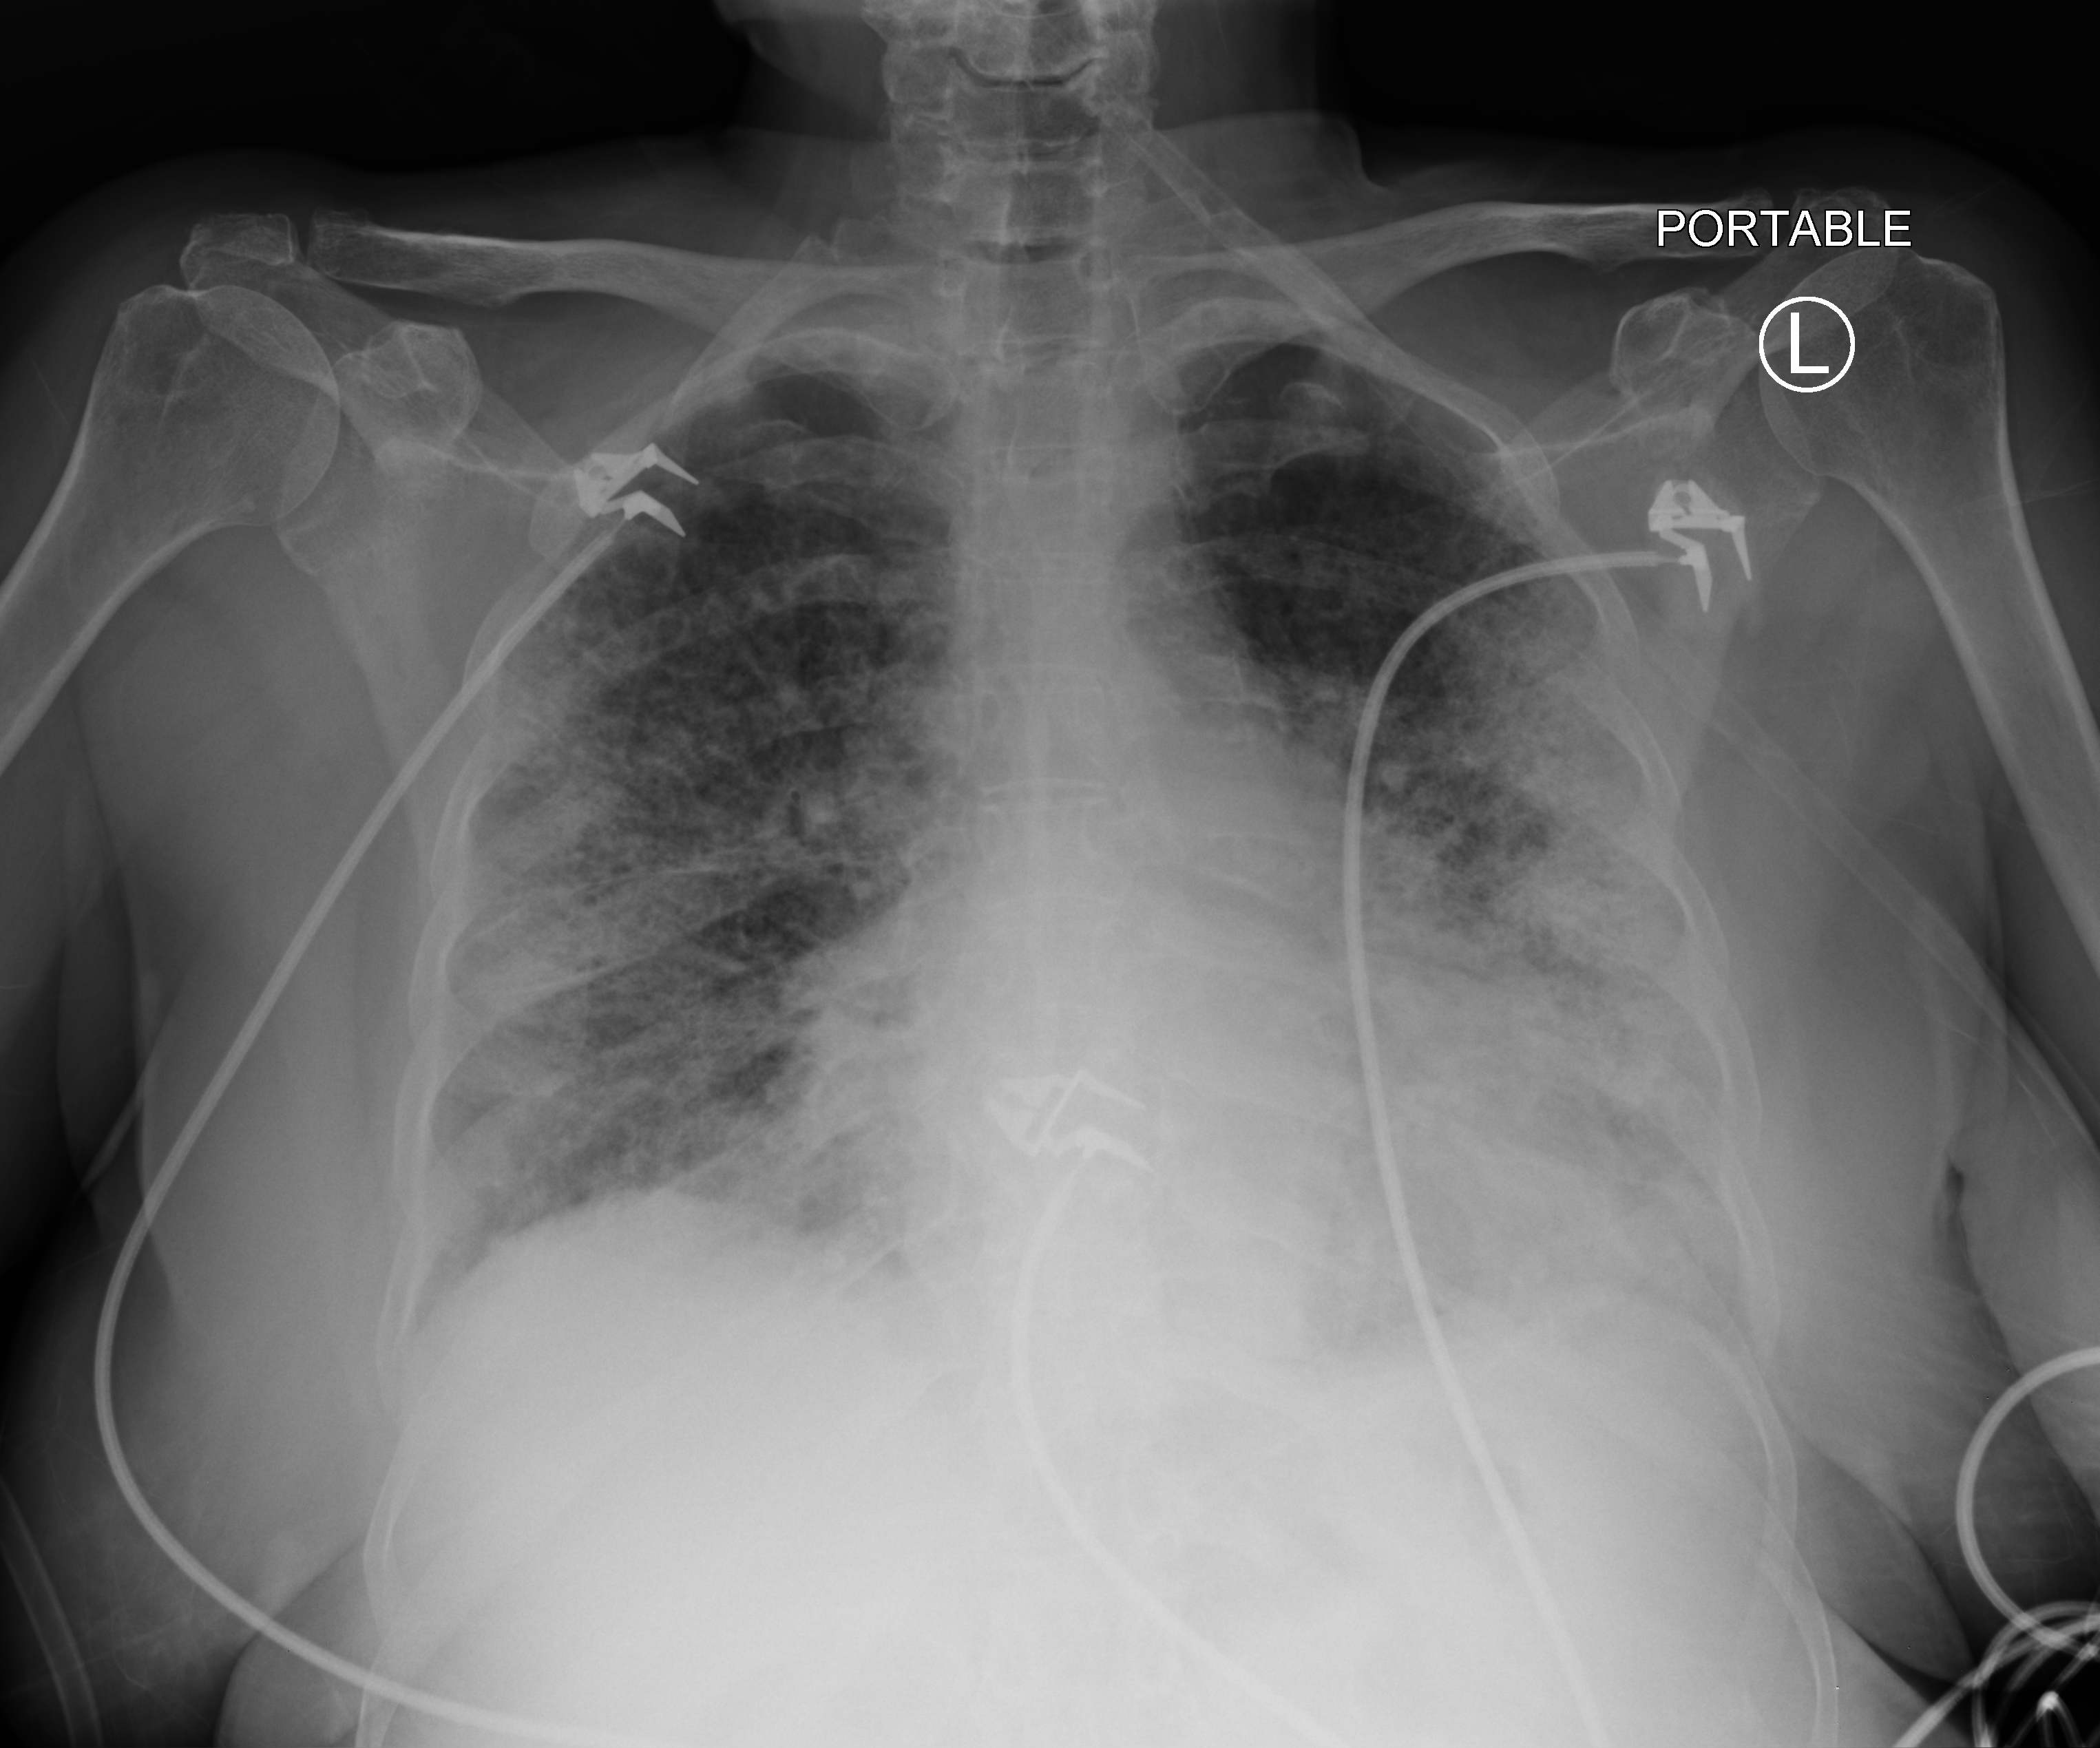
Portable chest radiograph, anteroposterior (AP) projection. Patient hospitalised with COVID-19; female, aged 60–74 years.
Hospital-stay facts (about this admission, not read from this image; timing relative to this image not recorded):
- COPD (admission record): no
- mechanically ventilated during this hospital stay: yes